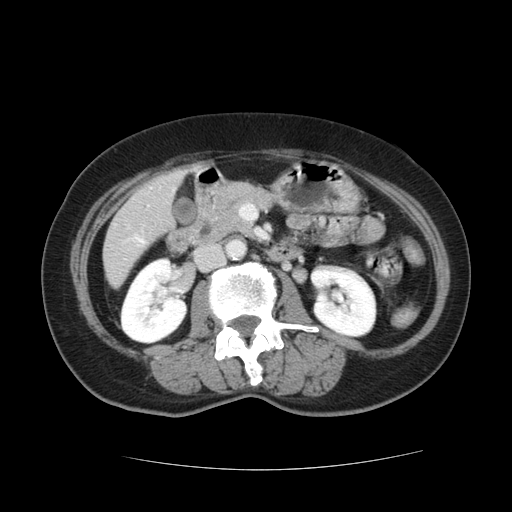
Contrast-enhanced abdominal CT, one axial slice. Position 36 of 128 along the scan axis. 120 kVp. Intravenous contrast given. Soft-tissue window (W 400 / L 40 HU). 2.5 mm slice thickness. 512 × 512 image matrix, field of view 366 × 366 mm. Female patient, age 67 years. From the clinical record (not read from this slice): diagnosis: colorectal cancer liver metastases, imaged before liver resection; multiple liver metastases: yes; largest metastasis: 3 cm.
Structures marked on this image (expert manual segmentation):
- liver: box from (x=104, y=173) to (x=181, y=285) px
- planned liver remnant (the part of the liver to remain after resection): (x=104, y=217)–(x=144, y=285)